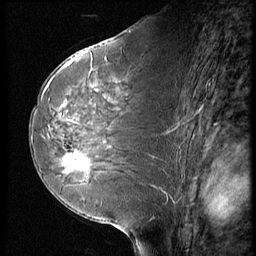
Breast MRI (dynamic contrast-enhanced), one sagittal slice. Slice 32 of 56 in the series (ordered by position). Dynamic contrast-enhanced series, image 2 of 3 at this slice position (ordered by acquisition). 1.5 T. TE 4.2 ms, TR 9 ms. 2.5 mm slice thickness. 256 × 256 image matrix. Female patient, age 58 years. Case-level facts recorded for this patient, not image findings: setting: breast cancer imaged before/during neoadjuvant chemotherapy; receptor status: HR-positive, HER2-negative.
Structures marked on this image (semi-automatic segmentation, software-assisted and operator-edited):
- analysis volume of interest (the breast-tissue region the enhancement analysis was run in; not a lesion): bounding box [x1, y1, x2, y2] px = [56, 146, 99, 182]
- tumour enhancement mask (voxels above the 140 % enhancement threshold inside the analysis volume of interest): [63, 152, 89, 172]